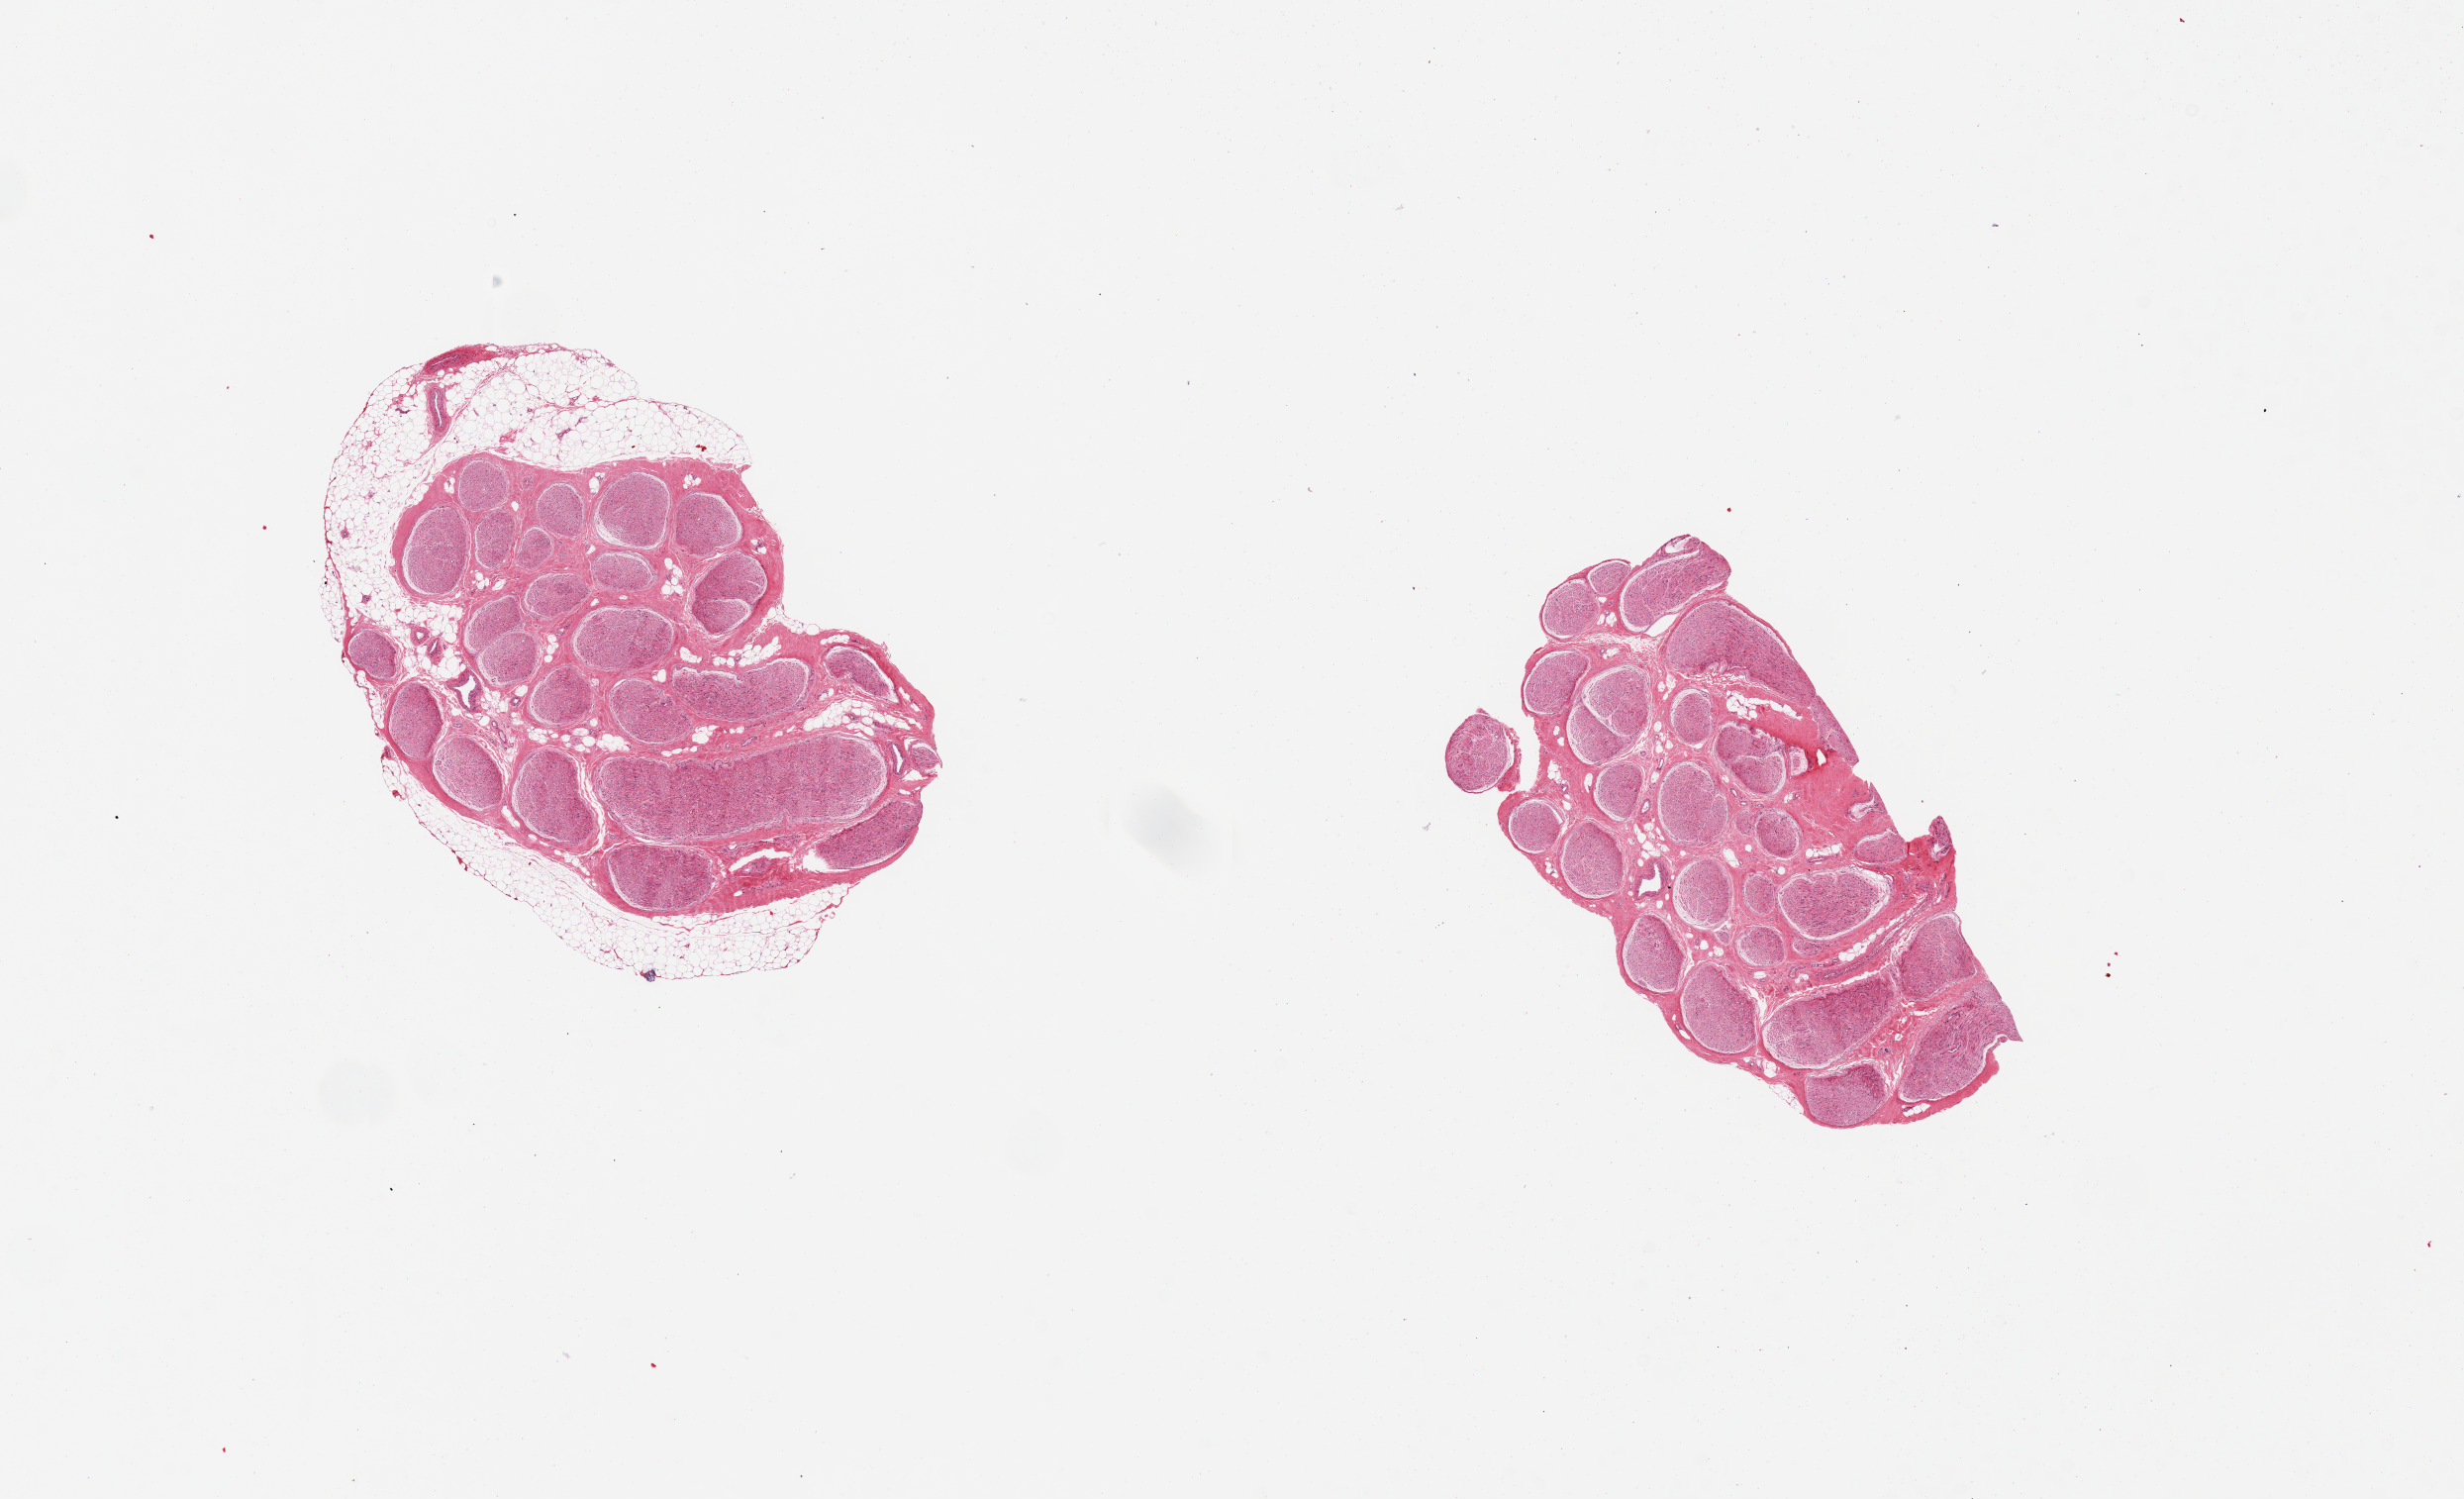
Digitized hematoxylin and eosin (H&E)-stained section, brightfield — low-resolution overview of the scanned area, about 19.7 x 12.0 mm. Donor sex: female.
• specimen: PAXgene-fixed, paraffin-embedded tissue; sampled site (target tissue): tibial nerve; tissue donor sample